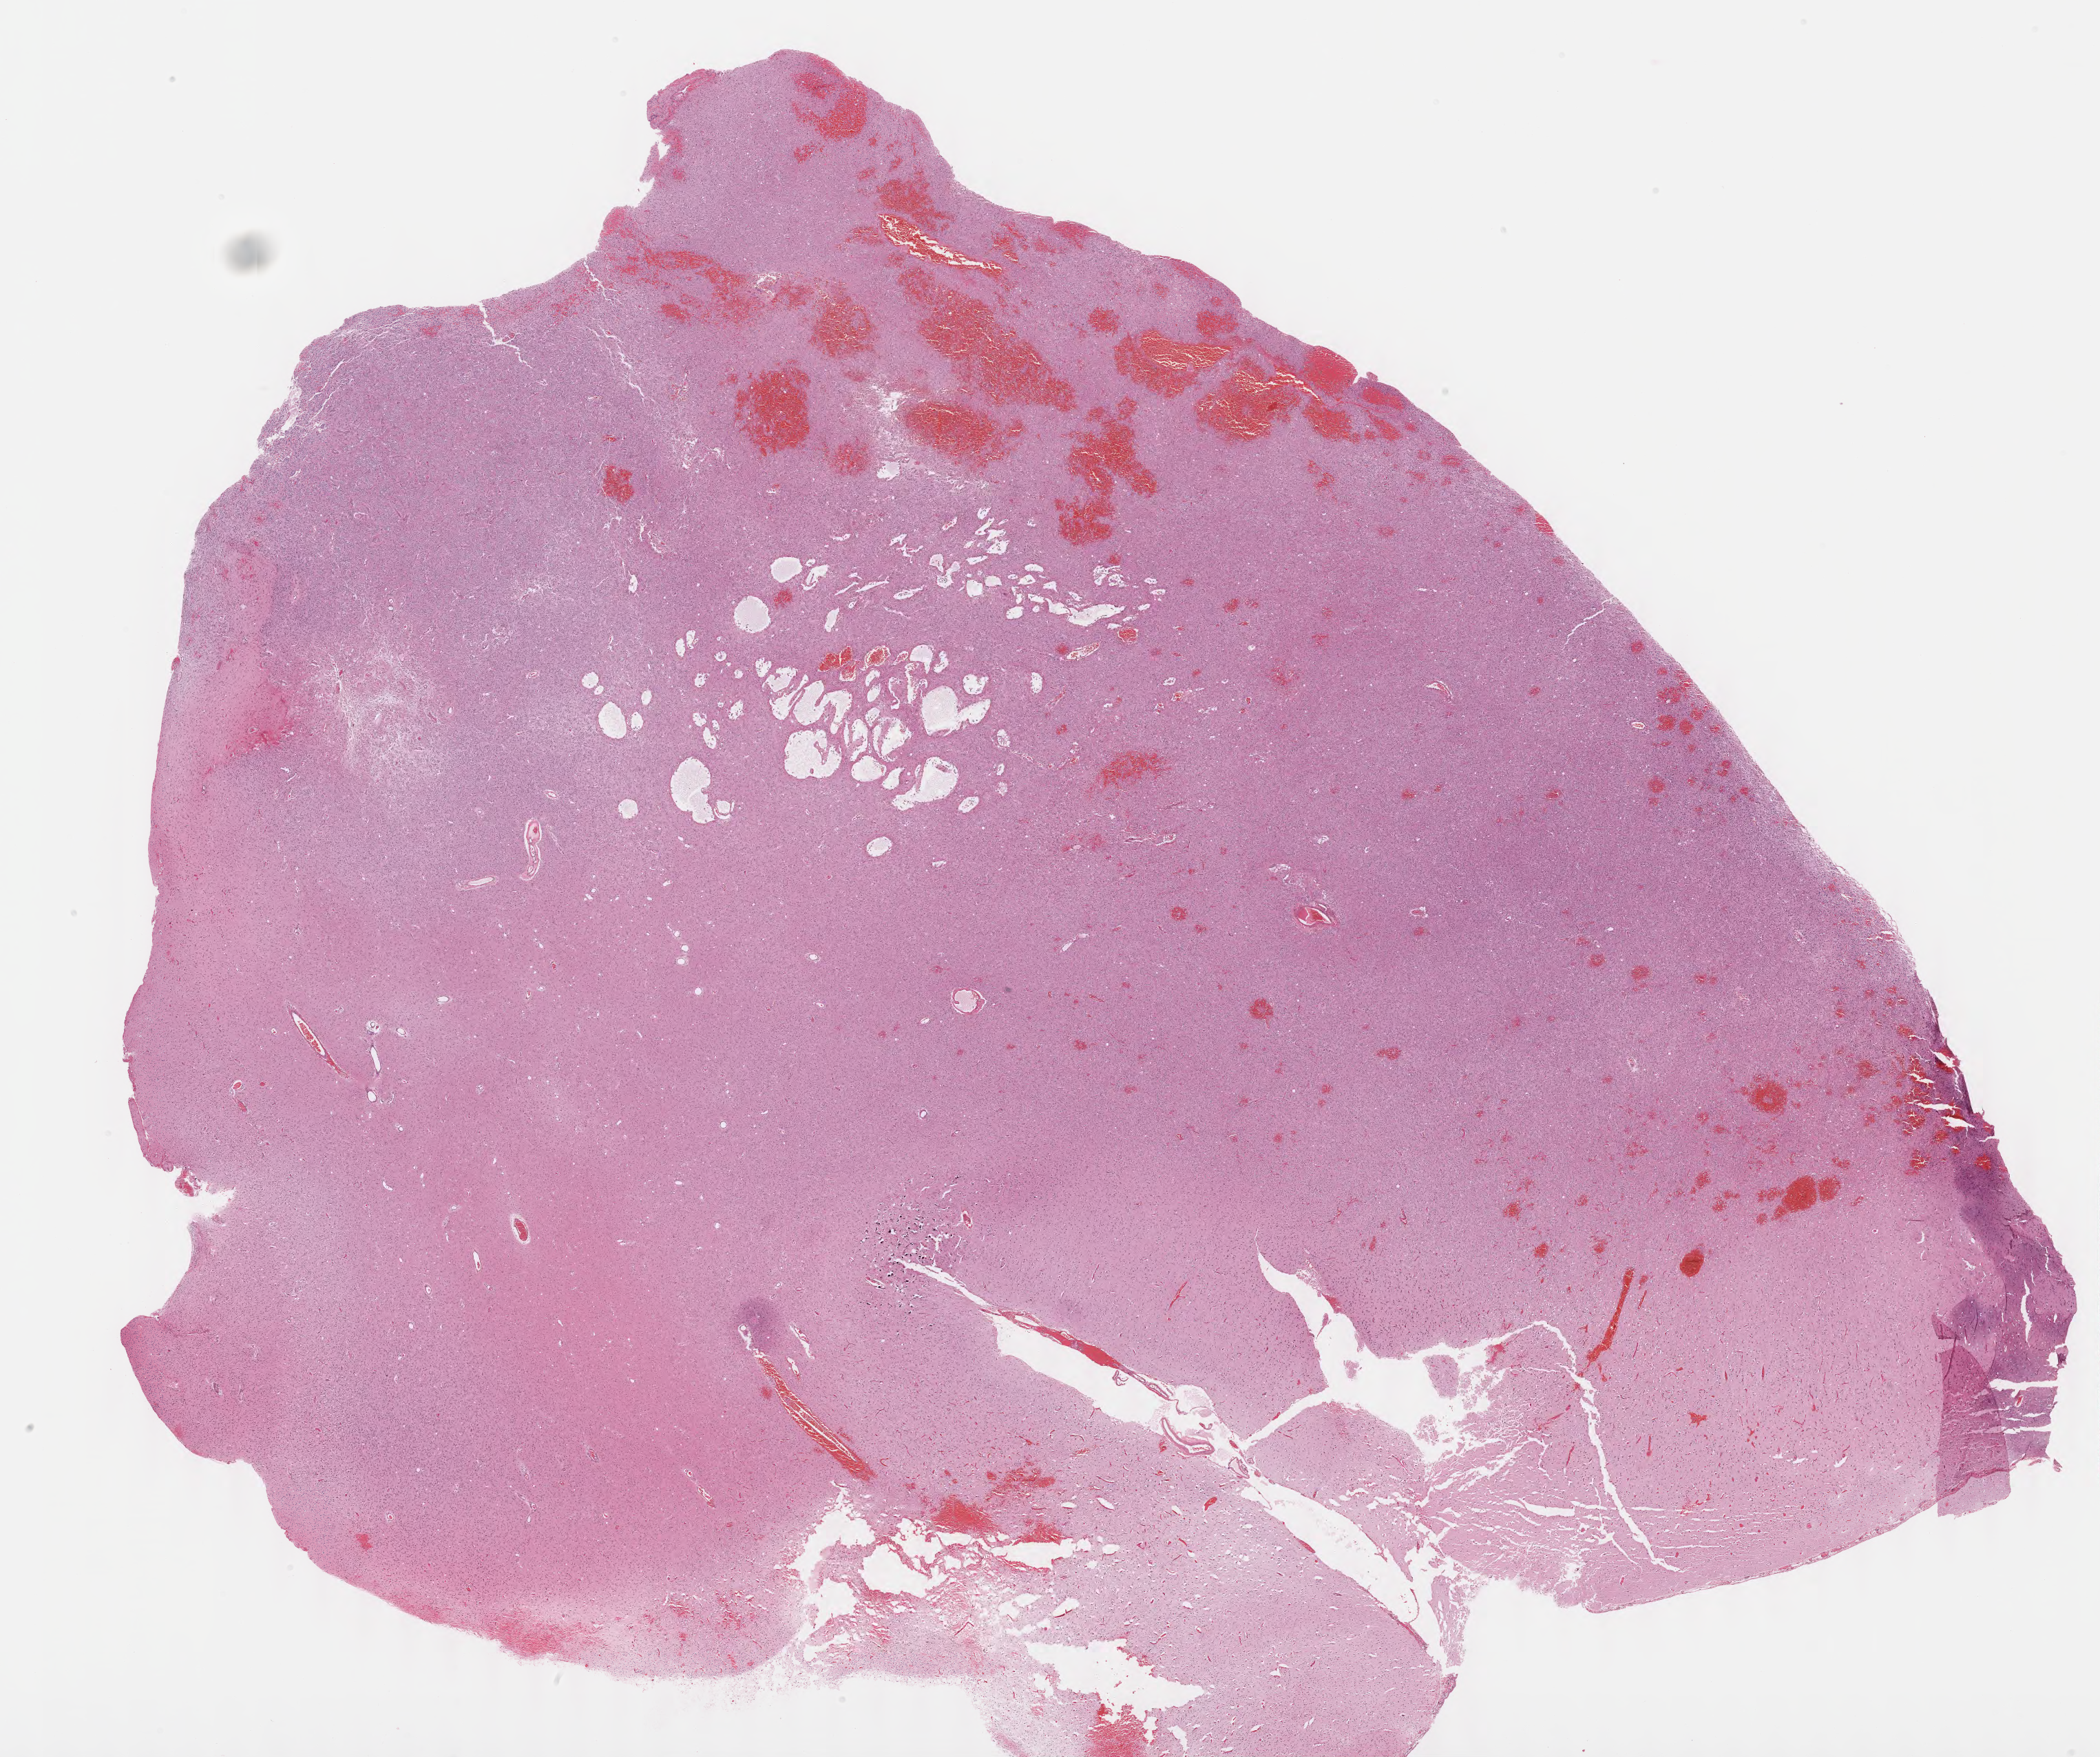
Whole-slide histology image, H&E-stained — shown as a low-resolution overview of the whole scanned area (about 24.1 x 20.2 mm, acquisition: 40x scan). Formalin-fixed paraffin-embedded (FFPE) diagnostic section. Sample: primary tumour, brain. Female, age 31 years at initial diagnosis. Histologic grade: G2 (moderately differentiated).
Diagnosis: Mixed glioma (cerebrum).